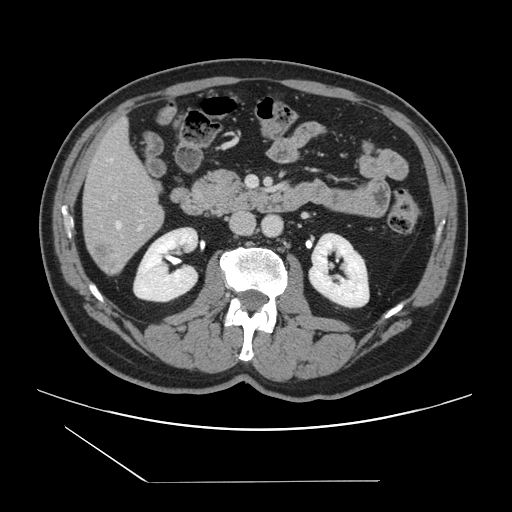
Contrast-enhanced abdominal CT, one axial slice; position 49 of 157 along the scan axis; 120 kVp; soft-tissue window (W 400 / L 40 HU); 2.5 mm slice thickness; 512 × 512 image matrix, field of view 407 × 407 mm. Male patient, age 61 years. Case-level facts recorded for this patient, not image findings: diagnosis: colorectal cancer liver metastases, imaged before liver resection; multiple liver metastases: yes; largest metastasis: 5.5 cm; chemotherapy before resection: no.
Structures marked on this image (manually delineated by an expert):
- hepatic veins: bounding box [x1, y1, x2, y2] px = [110, 159, 122, 229]
- liver: [83, 122, 163, 274]
- planned liver remnant (the part of the liver to remain after resection): [84, 122, 160, 218]
- portal vein (with intrahepatic branches): [114, 196, 142, 228]
- liver metastasis: [94, 243, 119, 273]